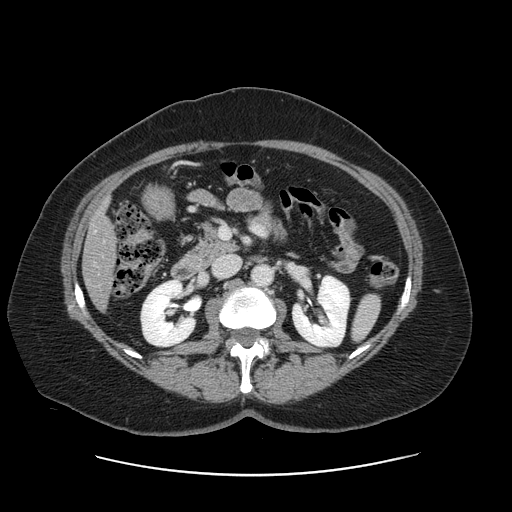
Contrast-enhanced abdominal CT, one axial slice. Position 55 of 161 along the scan axis. Intravenous contrast given. Soft-tissue window (W 400 / L 40 HU). 2.5 mm slice thickness. 512 × 512 image matrix, field of view 398 × 398 mm. Female patient, age 62 years. From the clinical record (not read from this slice): diagnosis: colorectal cancer liver metastases, imaged before liver resection; multiple liver metastases: no; largest metastasis: 2.5 cm; chemotherapy before resection: yes.
Structures marked on this image (outlined manually by an expert reader):
- liver: bounding box <84,208,115,307> (left, top, right, bottom; pixels)